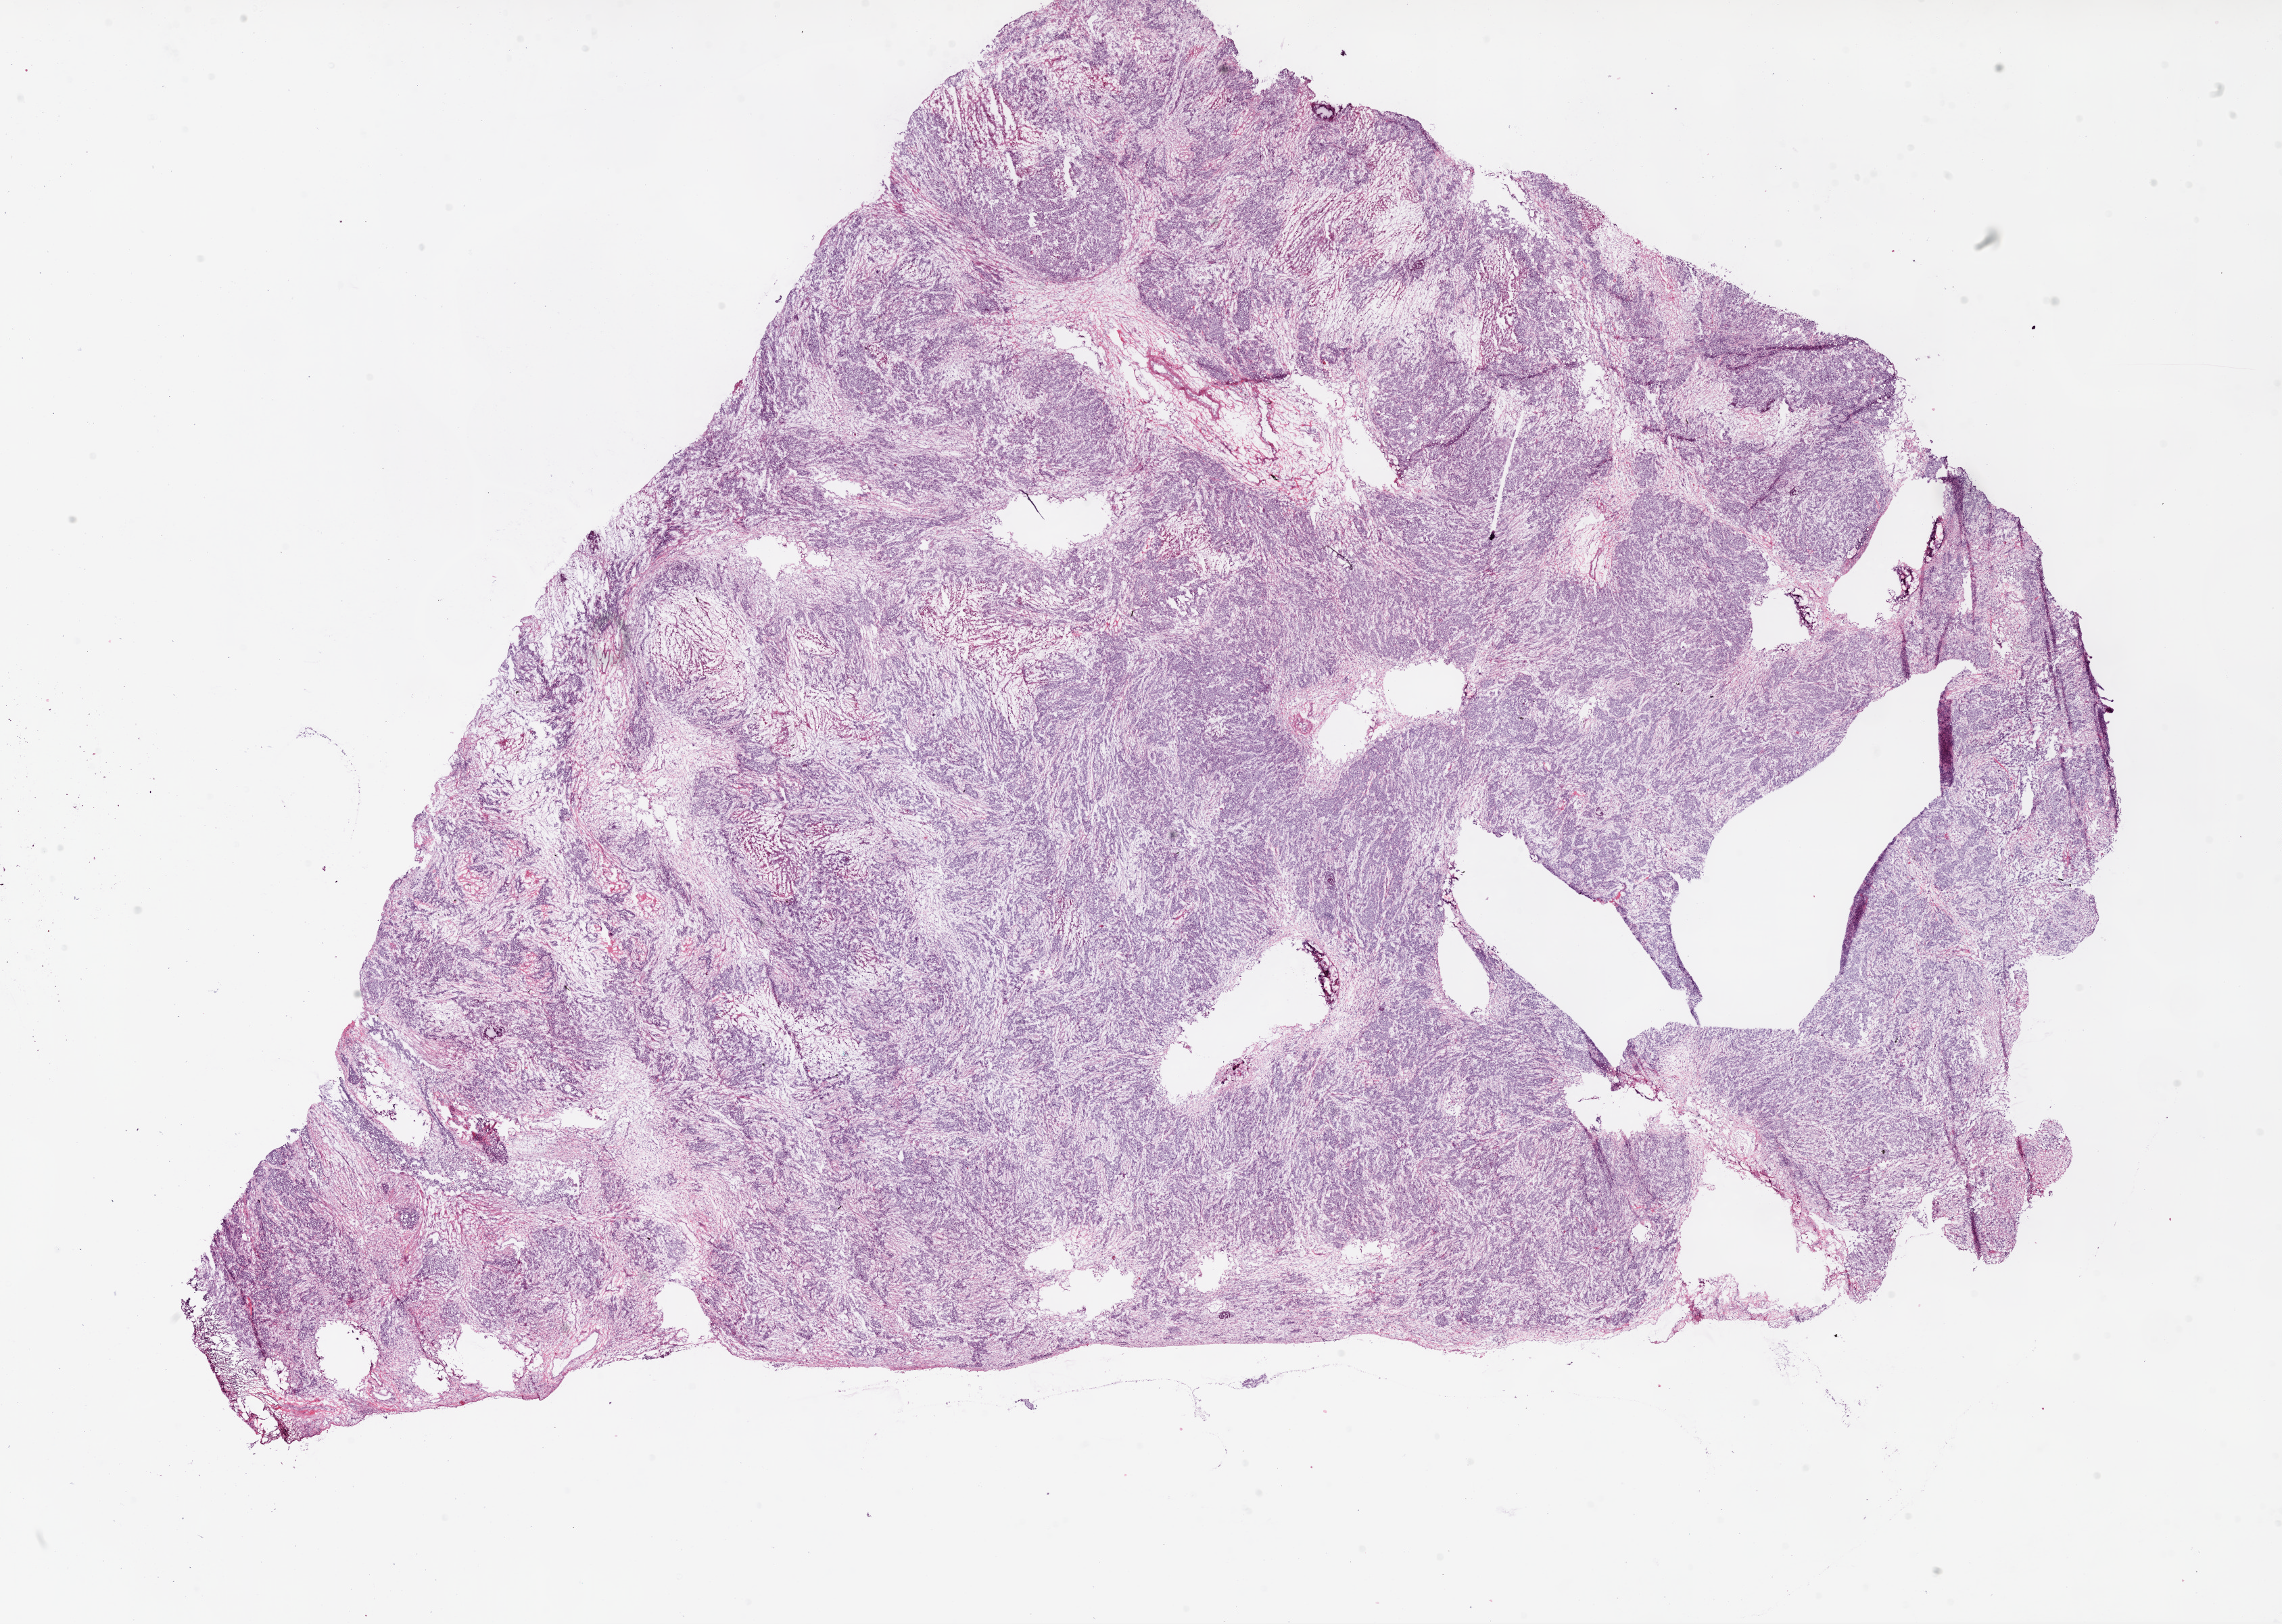
H&E-stained whole-slide image — whole scanned area (about 27.1 x 19.3 mm) shown as a low-resolution overview; frozen section from the bottom of the tissue portion; primary tumour sample from the ovary. Patient: female, age at initial diagnosis 63 years. Histologic grade: G3 (poorly differentiated). Pathologist review of this section (percent, as recorded): tumour cells 55%, tumour nuclei 80%, normal cells 0%, stromal cells 35%, necrosis 10%.
FIGO stage: IIIC. Pathologic diagnosis: Serous cystadenocarcinoma, NOS.